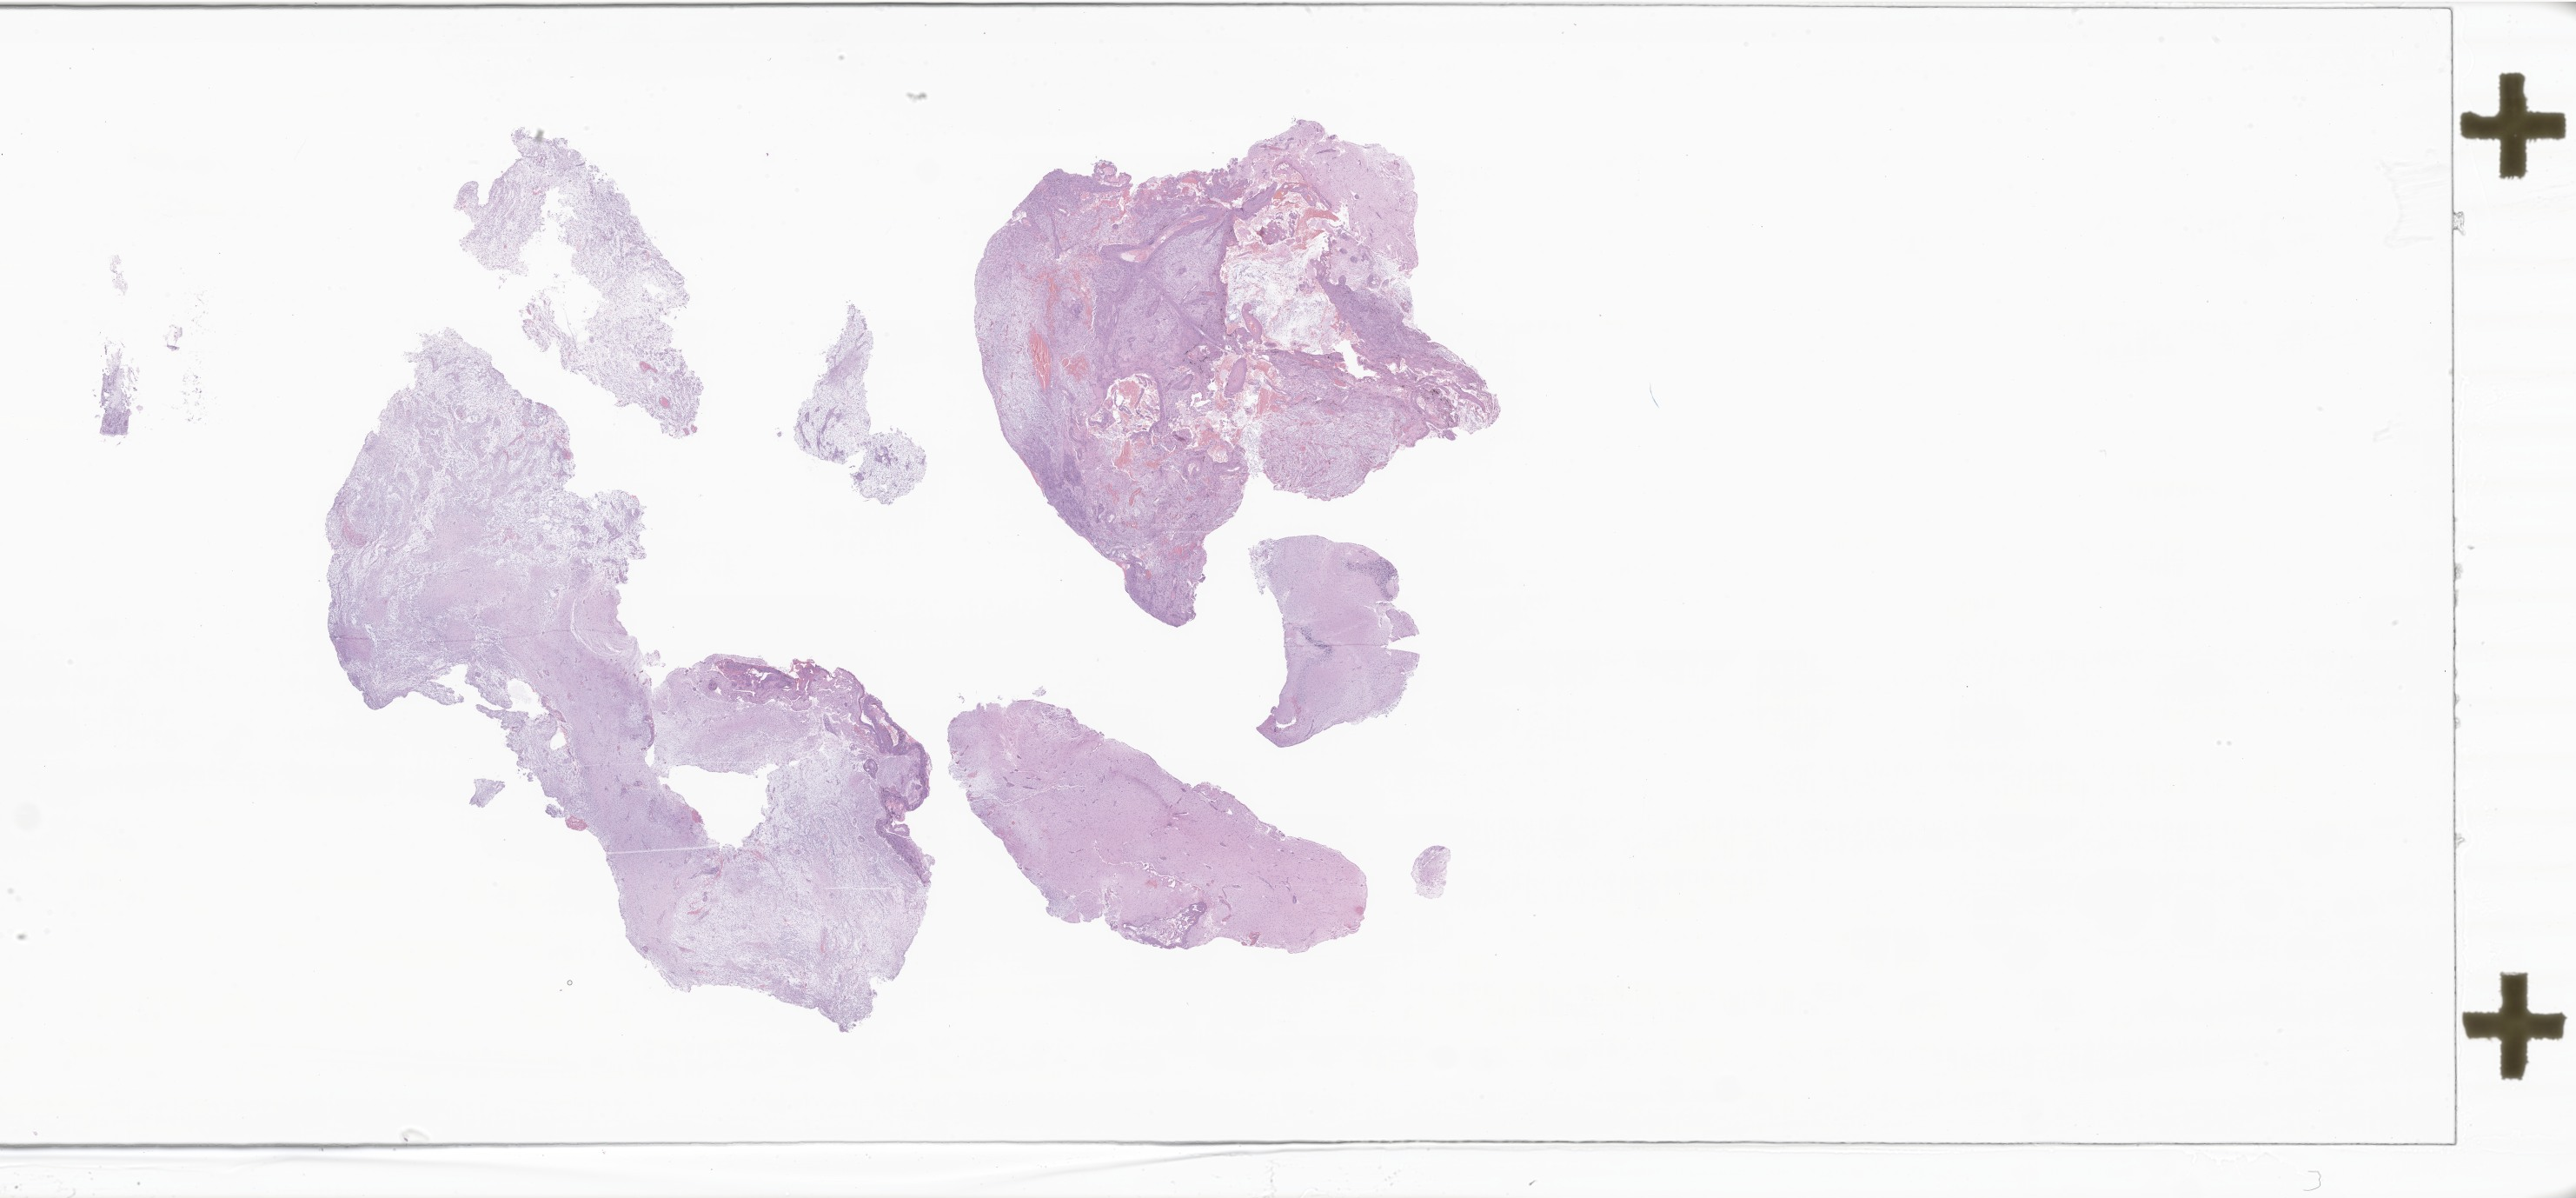
Digitized haematoxylin and eosin-stained section of tumor tissue from the brain — low-resolution overview of the scanned area, about 50.0 x 23.2 mm. Formalin-fixed, paraffin-embedded (FFPE) tissue. Patient: male, age 95 months (7 years 11 months).
Recorded diagnosis: Pilocytic astrocytoma.